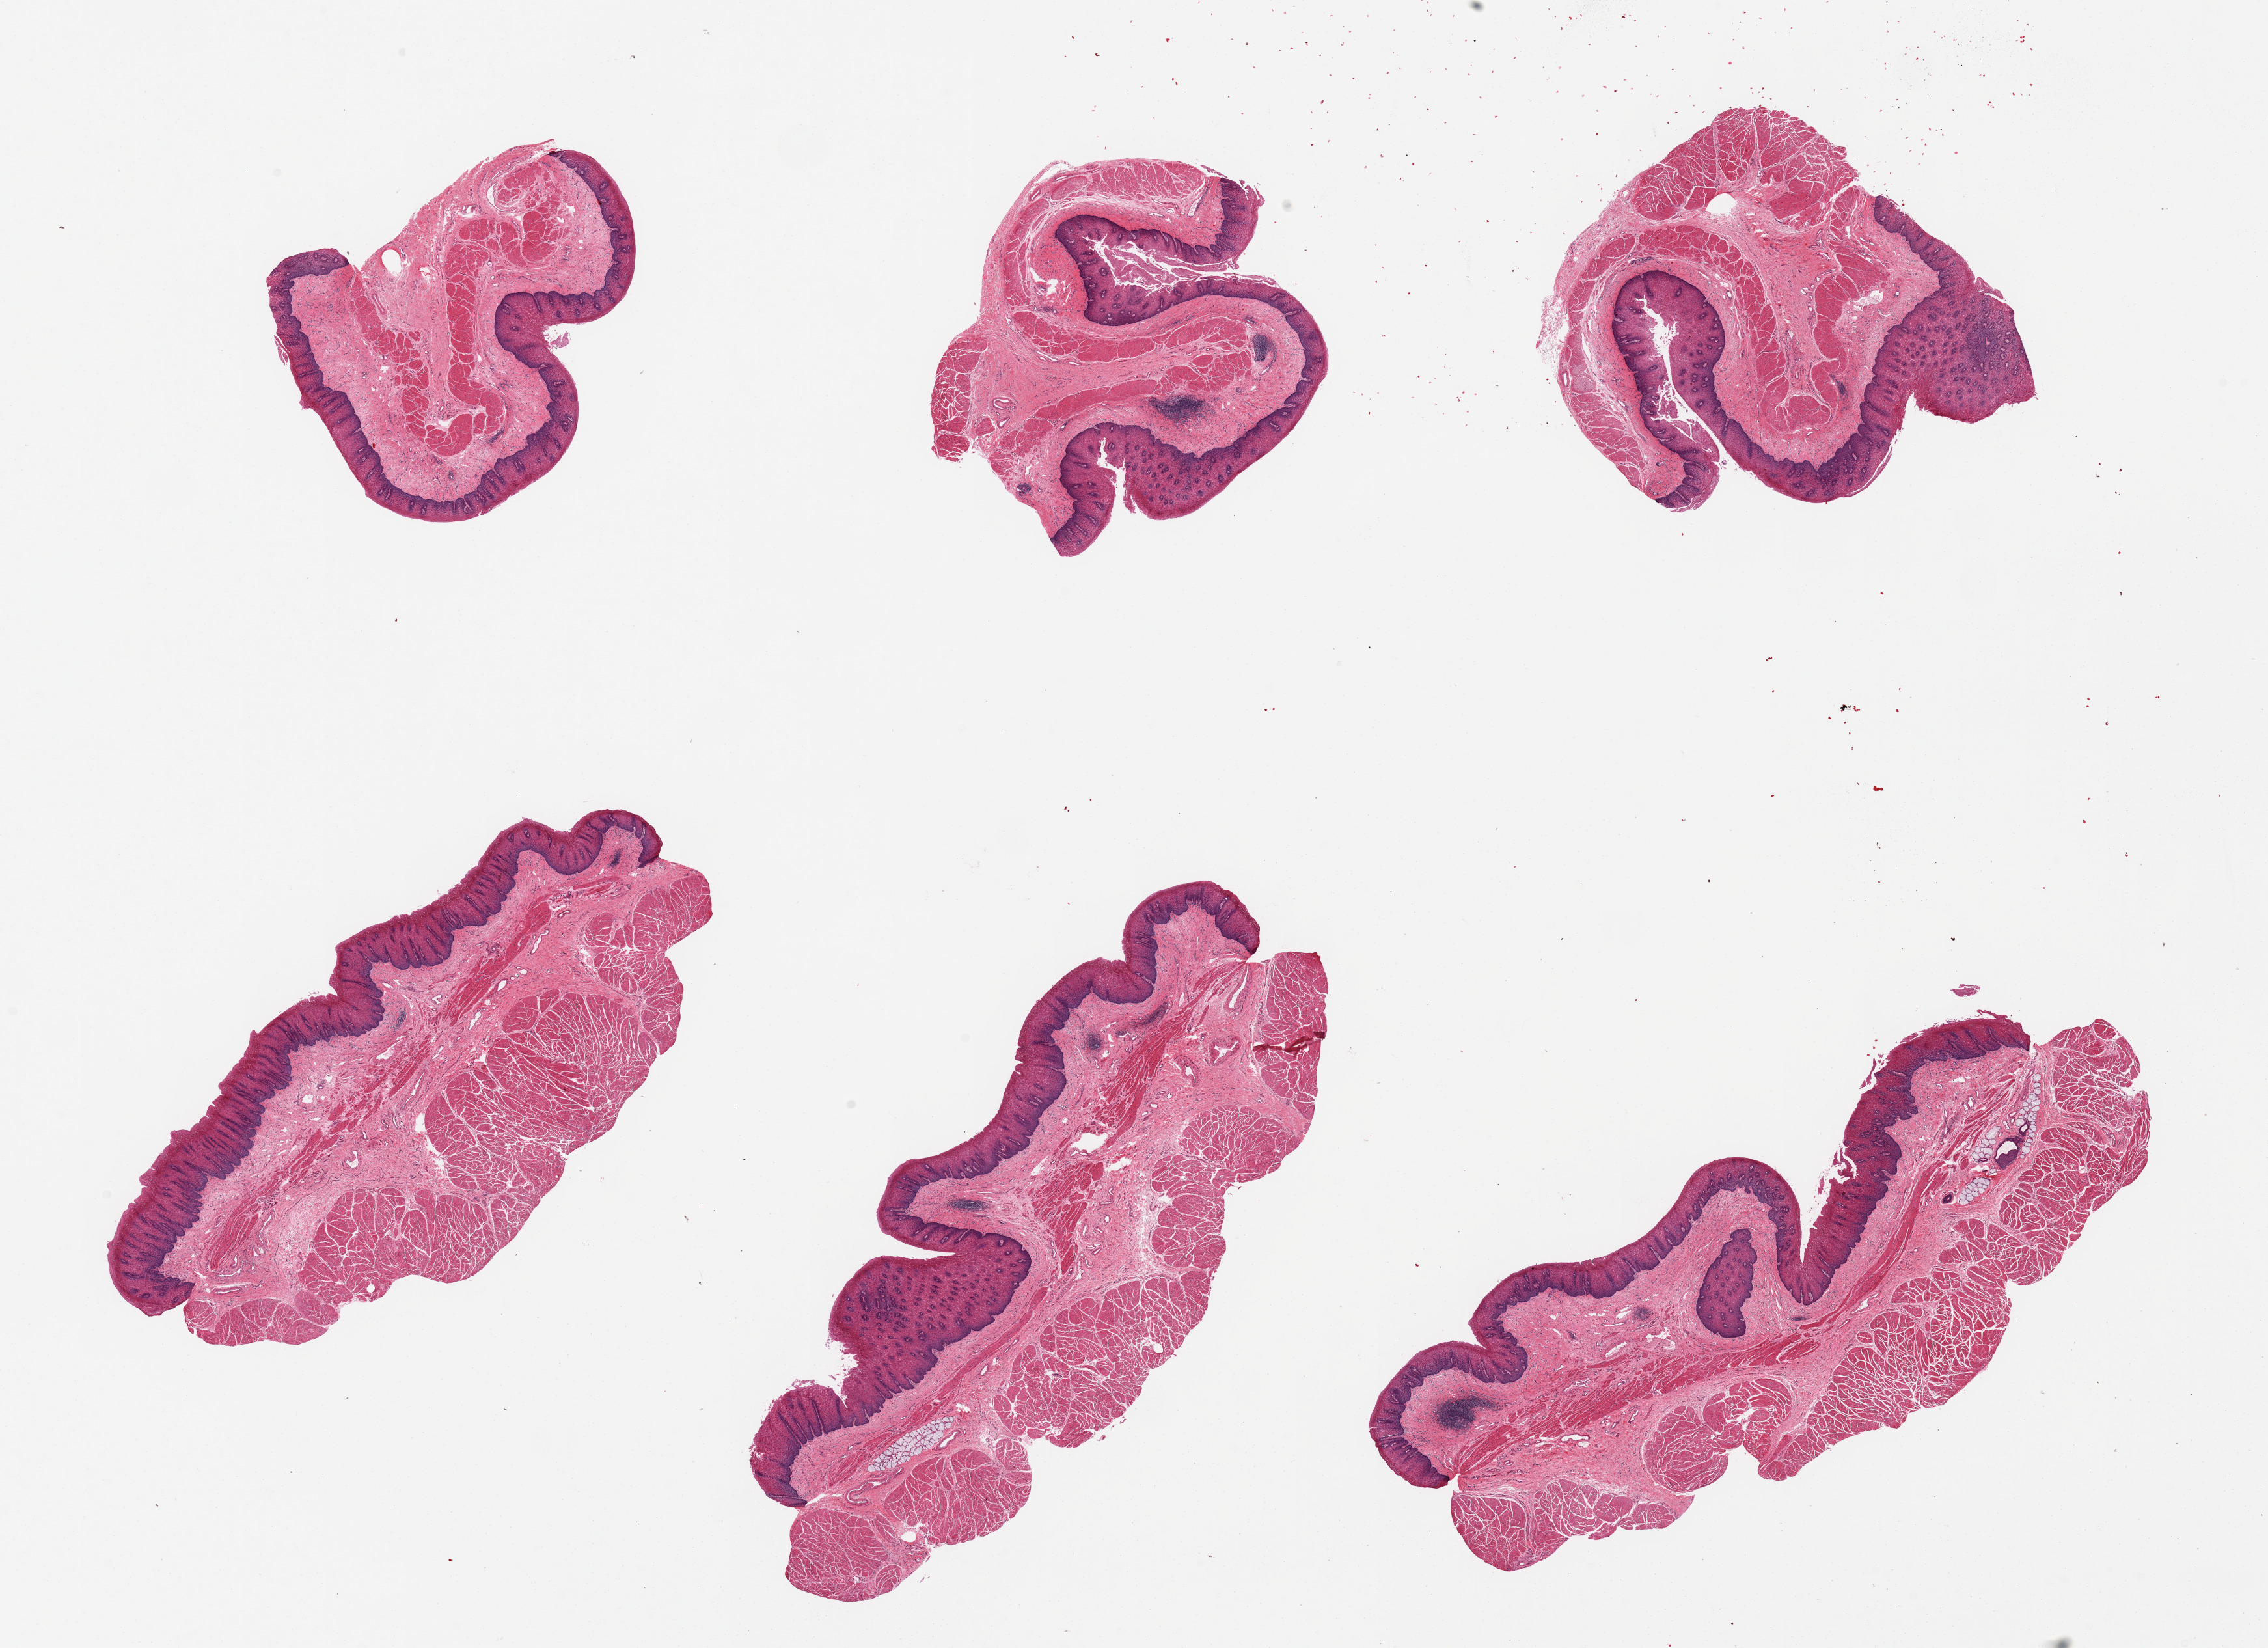
Digitized haematoxylin and eosin-stained section, low-resolution overview of the scanned area, about 27.6 x 20.0 mm (slide scanned at 20x); PAXgene-fixed, paraffin-embedded tissue; sampled site (target tissue): esophageal mucous membrane; donor tissue sample. Female donor.
Reviewer comment on this tissue sample: 6 pieces, several pieces include muscularis (not target), submucosal glands (some).